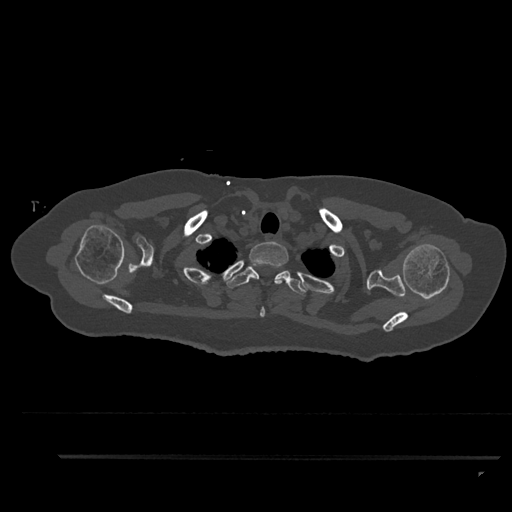
CT including the spine, one axial slice; position 740 of 797 along the scan axis; bone window (W 1800 / L 400 HU); 0.5 mm slice thickness; 512 × 512 image matrix, field of view 408 × 408 mm. Female patient, age 44 years. From the clinical record (not read from this slice): primary cancer: renal; vertebrae with lytic lesions (as recorded): L1.
Annotated regions visible in this slice (semi-automatically segmented with operator editing):
- T1 vertebra: bounding box [x1, y1, x2, y2] px = [249, 241, 289, 317]
- T2 vertebra: [226, 264, 306, 295]